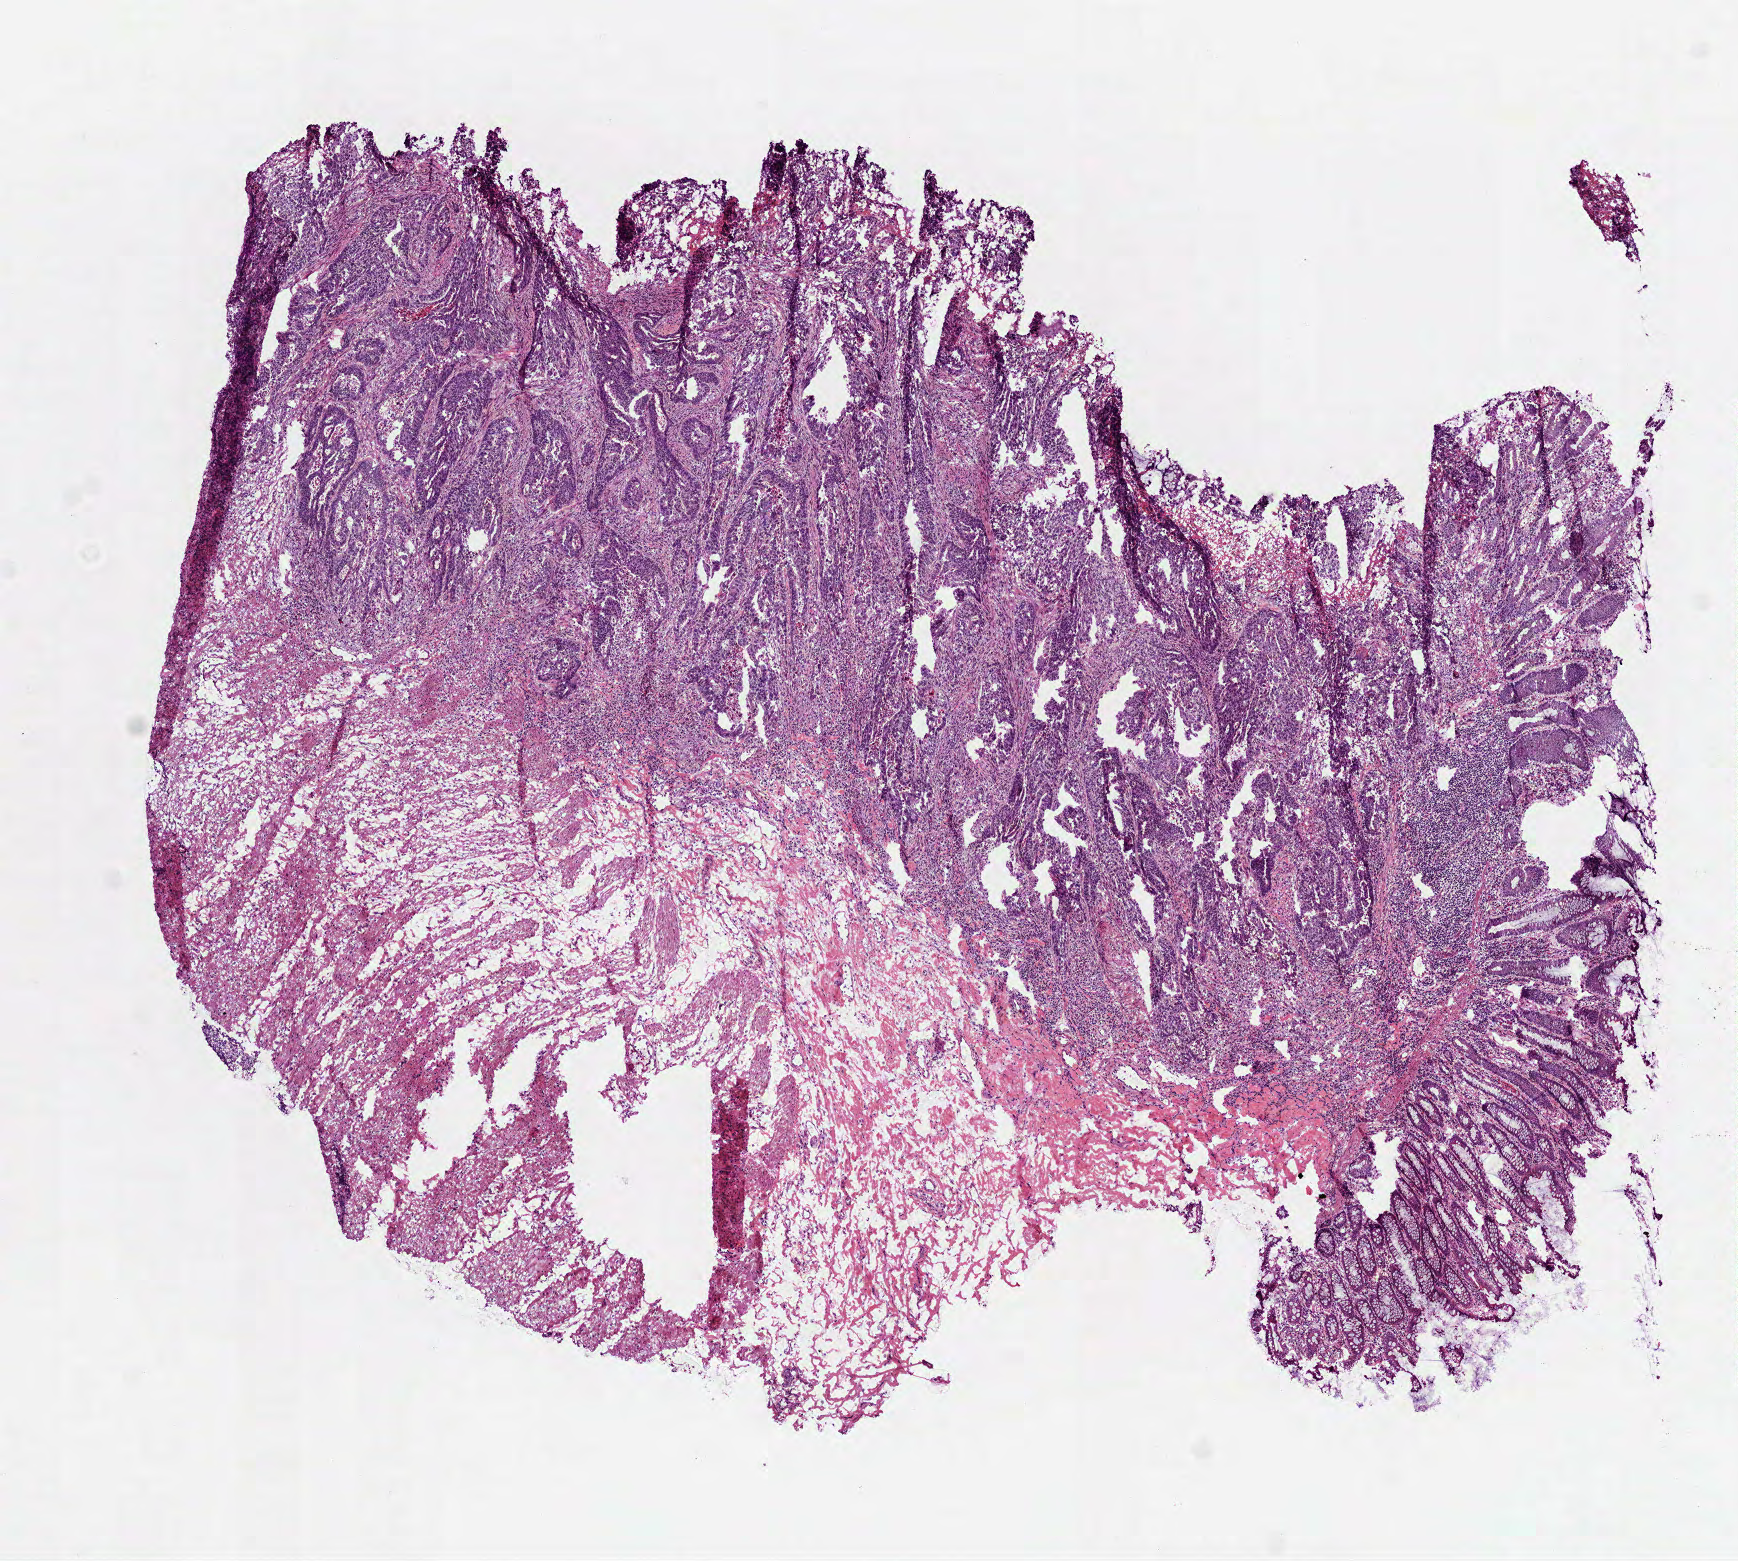
Whole-slide histology image, Hematoxylin and eosin (H&E) stained, whole scanned area (about 7.0 x 6.3 mm) shown as a low-resolution overview; frozen section from the top of the tissue portion; colon, primary tumour sample. Female, age 81 years at initial diagnosis. Composition of this section per pathologist review: tumour cells 60%, tumour nuclei 65%, normal cells 35%, necrosis 5%.
Lymph nodes positive (case pathology): 0 of 12 examined. AJCC pathologic stage: I. Pathologic diagnosis: Adenocarcinoma, NOS (splenic flexure of colon).